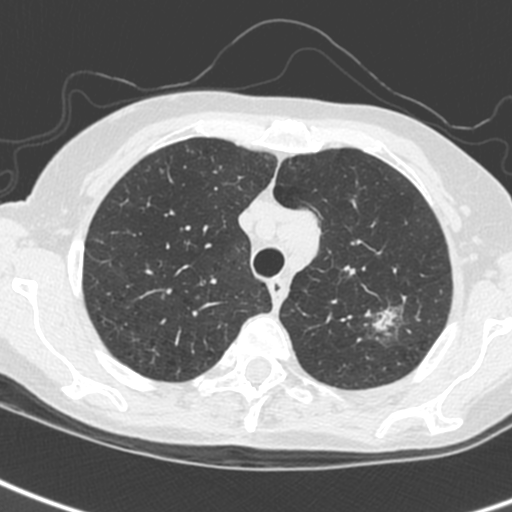
Chest CT (low-dose screening protocol), one axial image. First (baseline) screen. Lung window (W 1500 / L -600 HU). Standard (soft-tissue) reconstruction kernel (C). 120 kVp. Female participant, aged 61 years at enrolment.
Lesion marked by an expert reader, box from (x=350, y=301) to (x=412, y=350) px. The screening reader recorded 2 non-calcified nodules or masses ≥4 mm on this exam; which of them this box marks is not recorded. Official screen result: positive, change unspecified: nodule(s) >= 4 mm or enlarging nodule(s), mass(es), or other non-specific abnormalities suspicious for lung cancer. Later outcome: lung cancer diagnosed 29 days after this screen — small cell carcinoma, NOS, left upper lobe, stage IV (AJCC 6th edition).